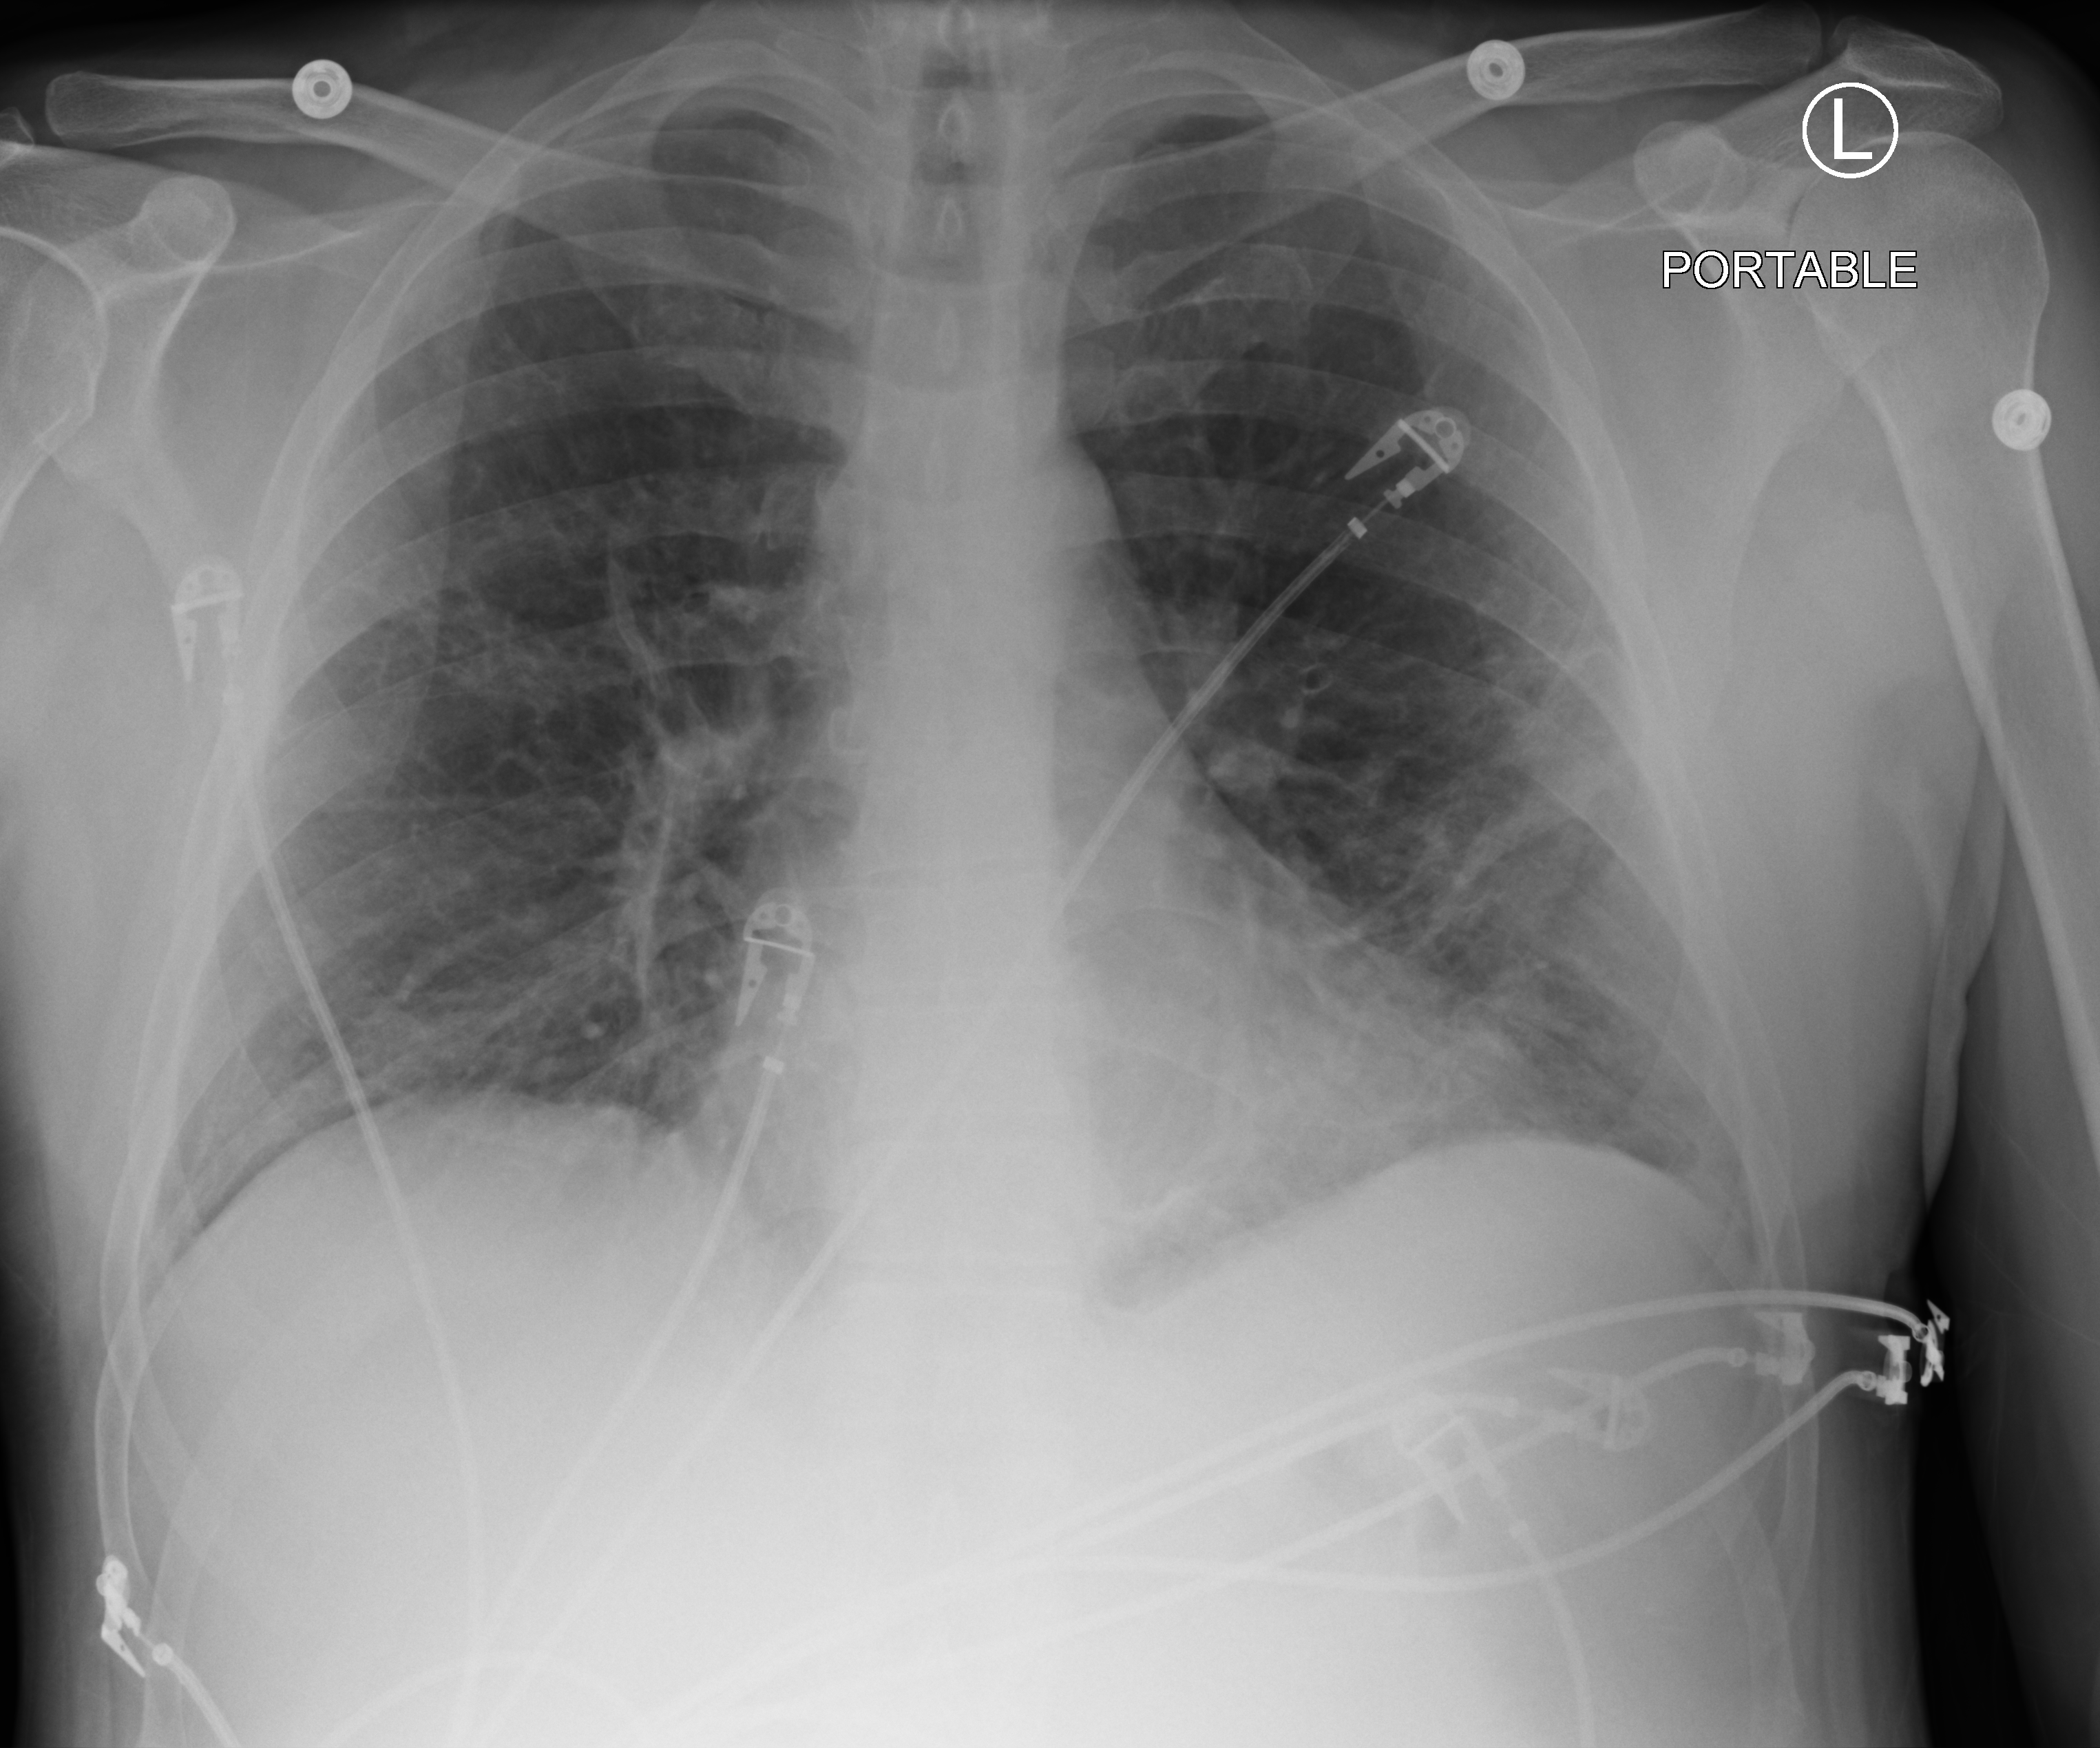
Chest X-ray (portable); anteroposterior (AP) projection. Male patient hospitalised with COVID-19, age 60–74 years.
Hospital-stay facts (about this admission, not read from this image; timing relative to this image not recorded): hypertension (admission record): no; chronic kidney disease (admission record): no.